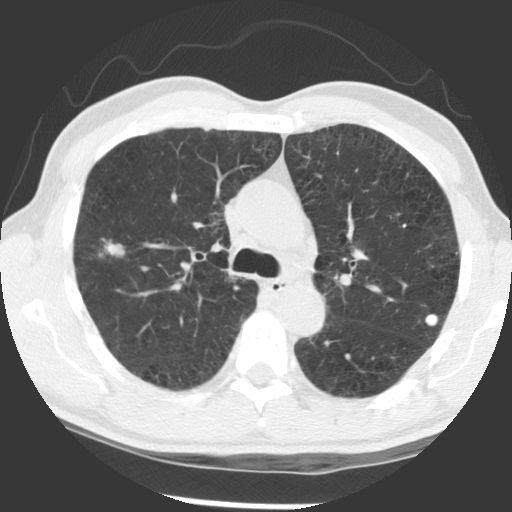
Chest CT (low-dose screening protocol), one axial image, baseline screening round, lung window (W 1500 / L -600 HU), slice 94 of 140 in the series. Male, age 56 years at enrolment.
Lesion marked by an expert reader, box from (x=64, y=224) to (x=131, y=276) px. Screening reader's record for this exam (one nodule recorded; not confirmed to be the boxed lesion): non-calcified nodule or mass ≥4 mm, right upper lobe, 12 × 7 mm, spiculated (stellate) margins, soft tissue attenuation. Later outcome: lung cancer diagnosed 676 days after this screen — squamous cell carcinoma, NOS, right upper lobe, right middle lobe, moderately differentiated (G2), stage IB (AJCC 6th edition), 70 mm at pathology.